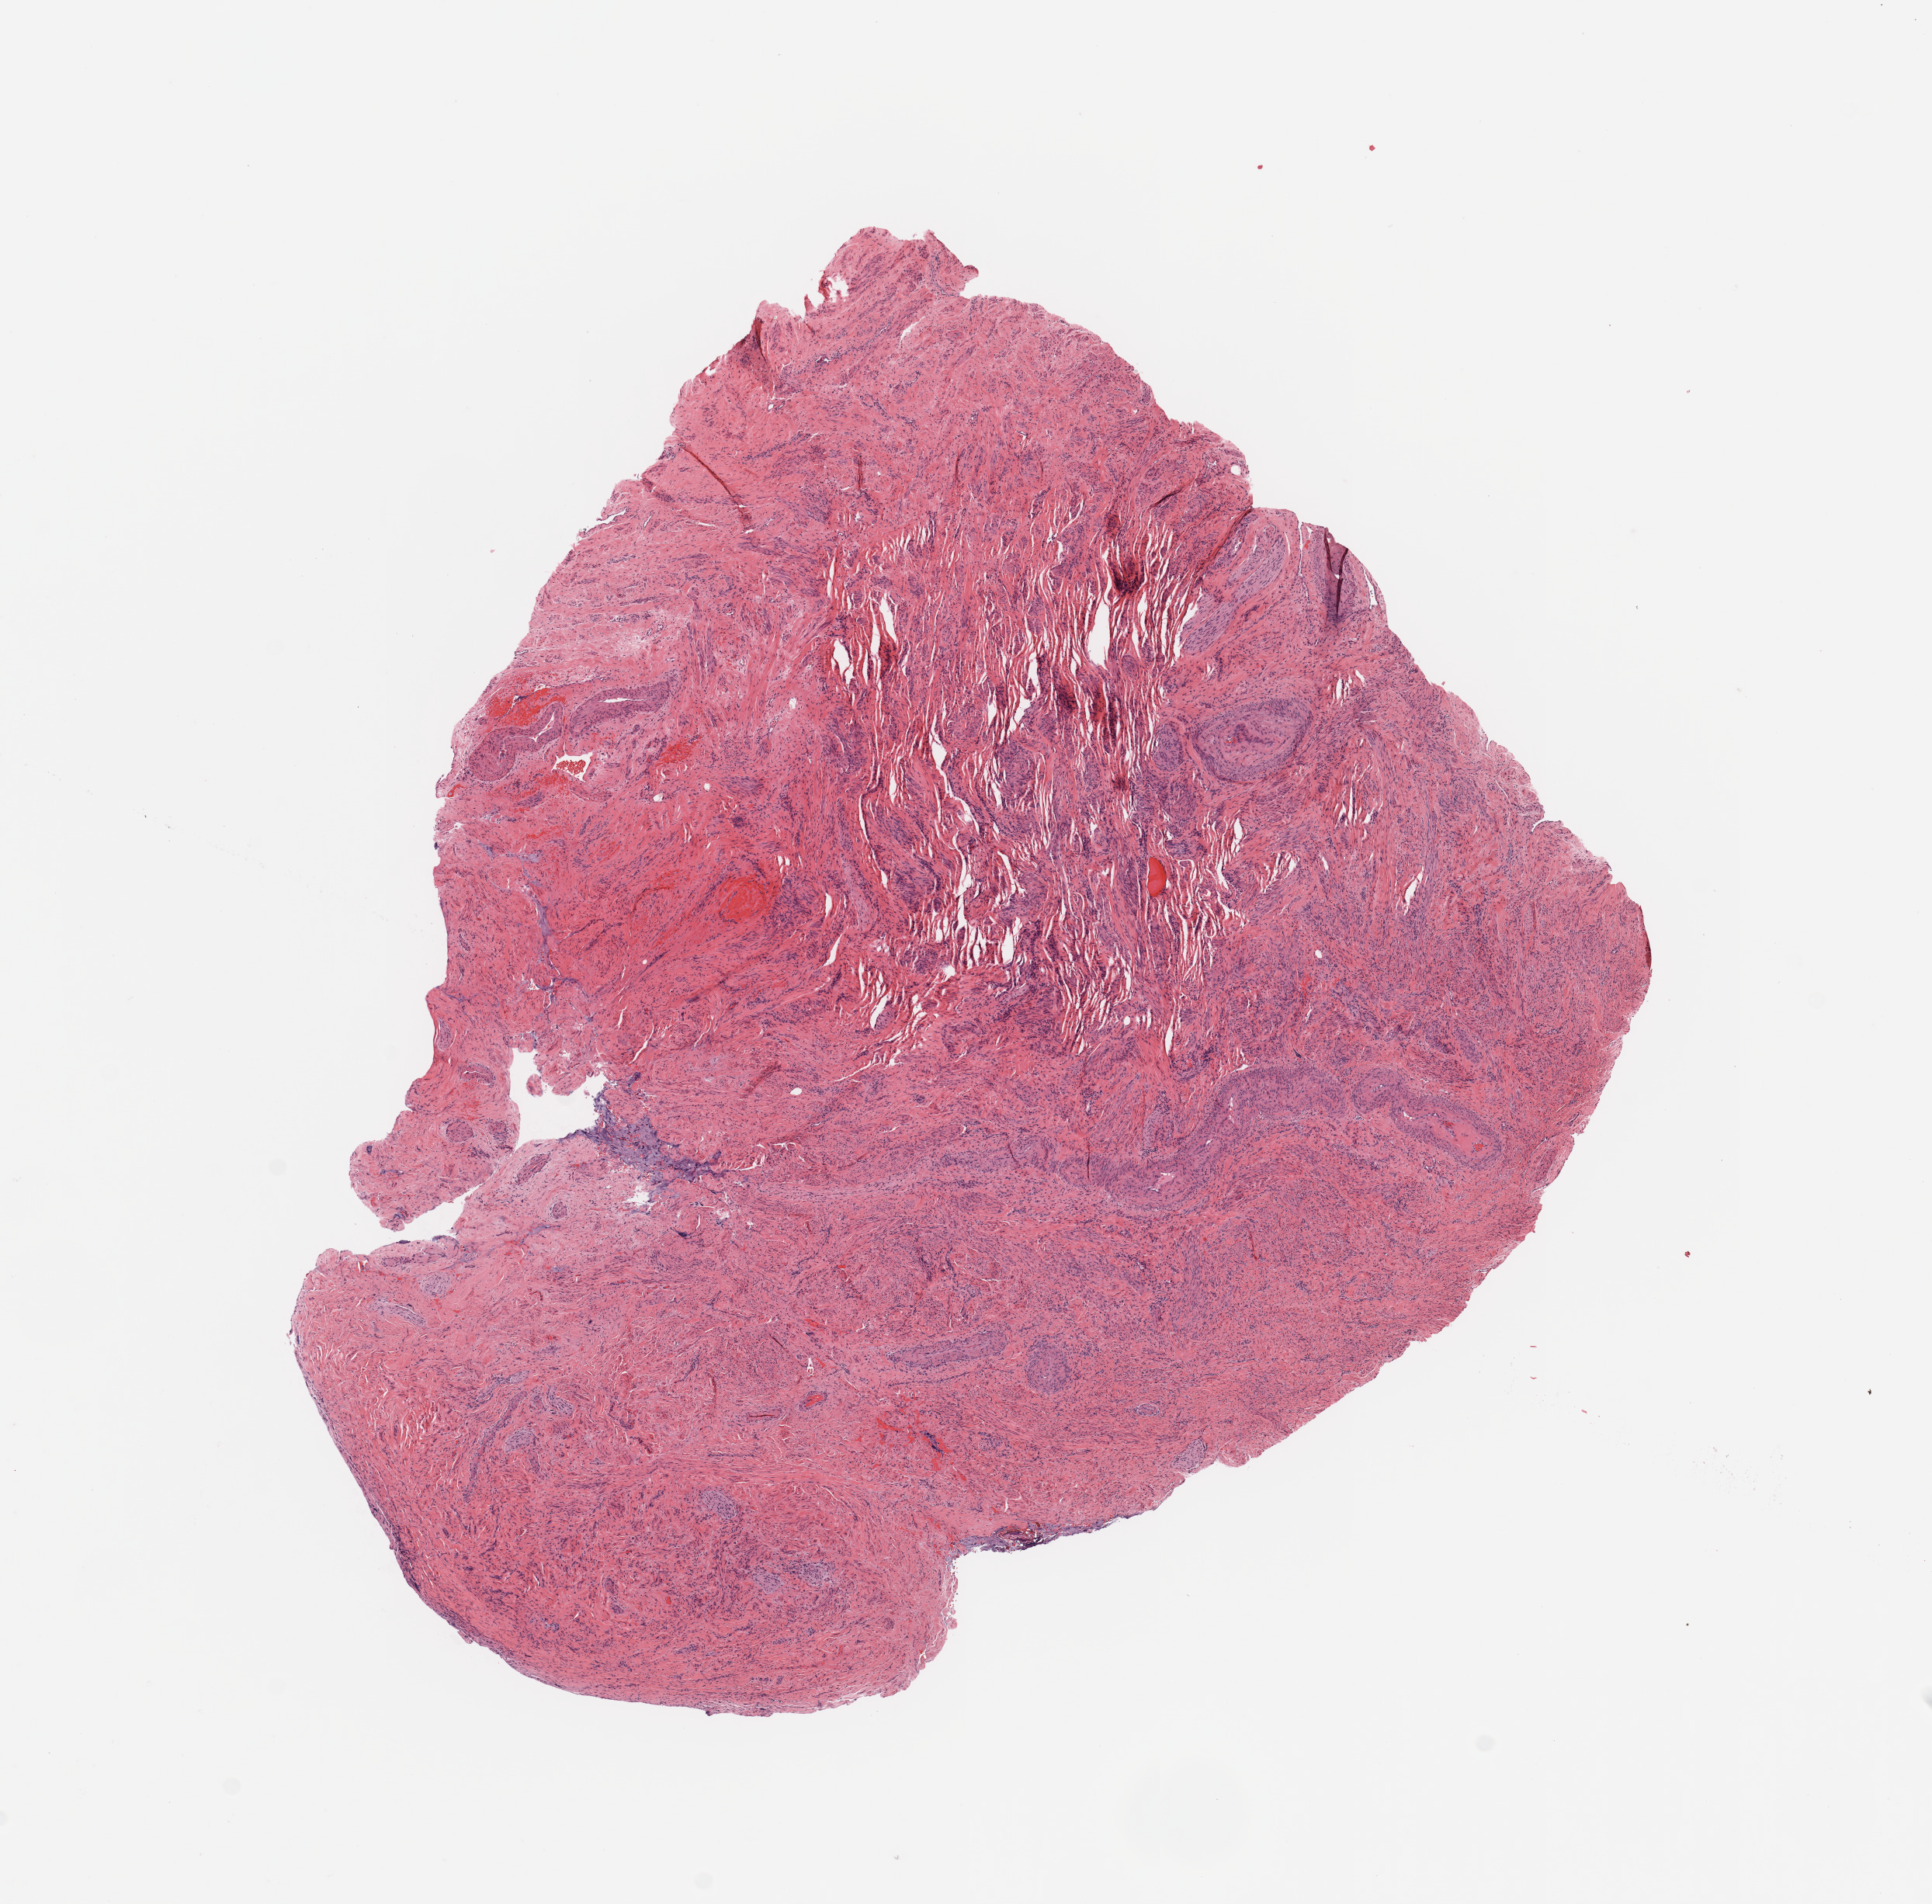
Digitized H&E-stained tissue section (whole slide), low-resolution overview of the scanned area, about 9.8 x 9.7 mm (acquisition: 20x scan); uterus, normal (non-tumour) tissue. 67-year-old female patient.
This section: normal (non-tumour) tissue from the same patient. Patient diagnosis: Endometrioid adenocarcinoma, NOS.